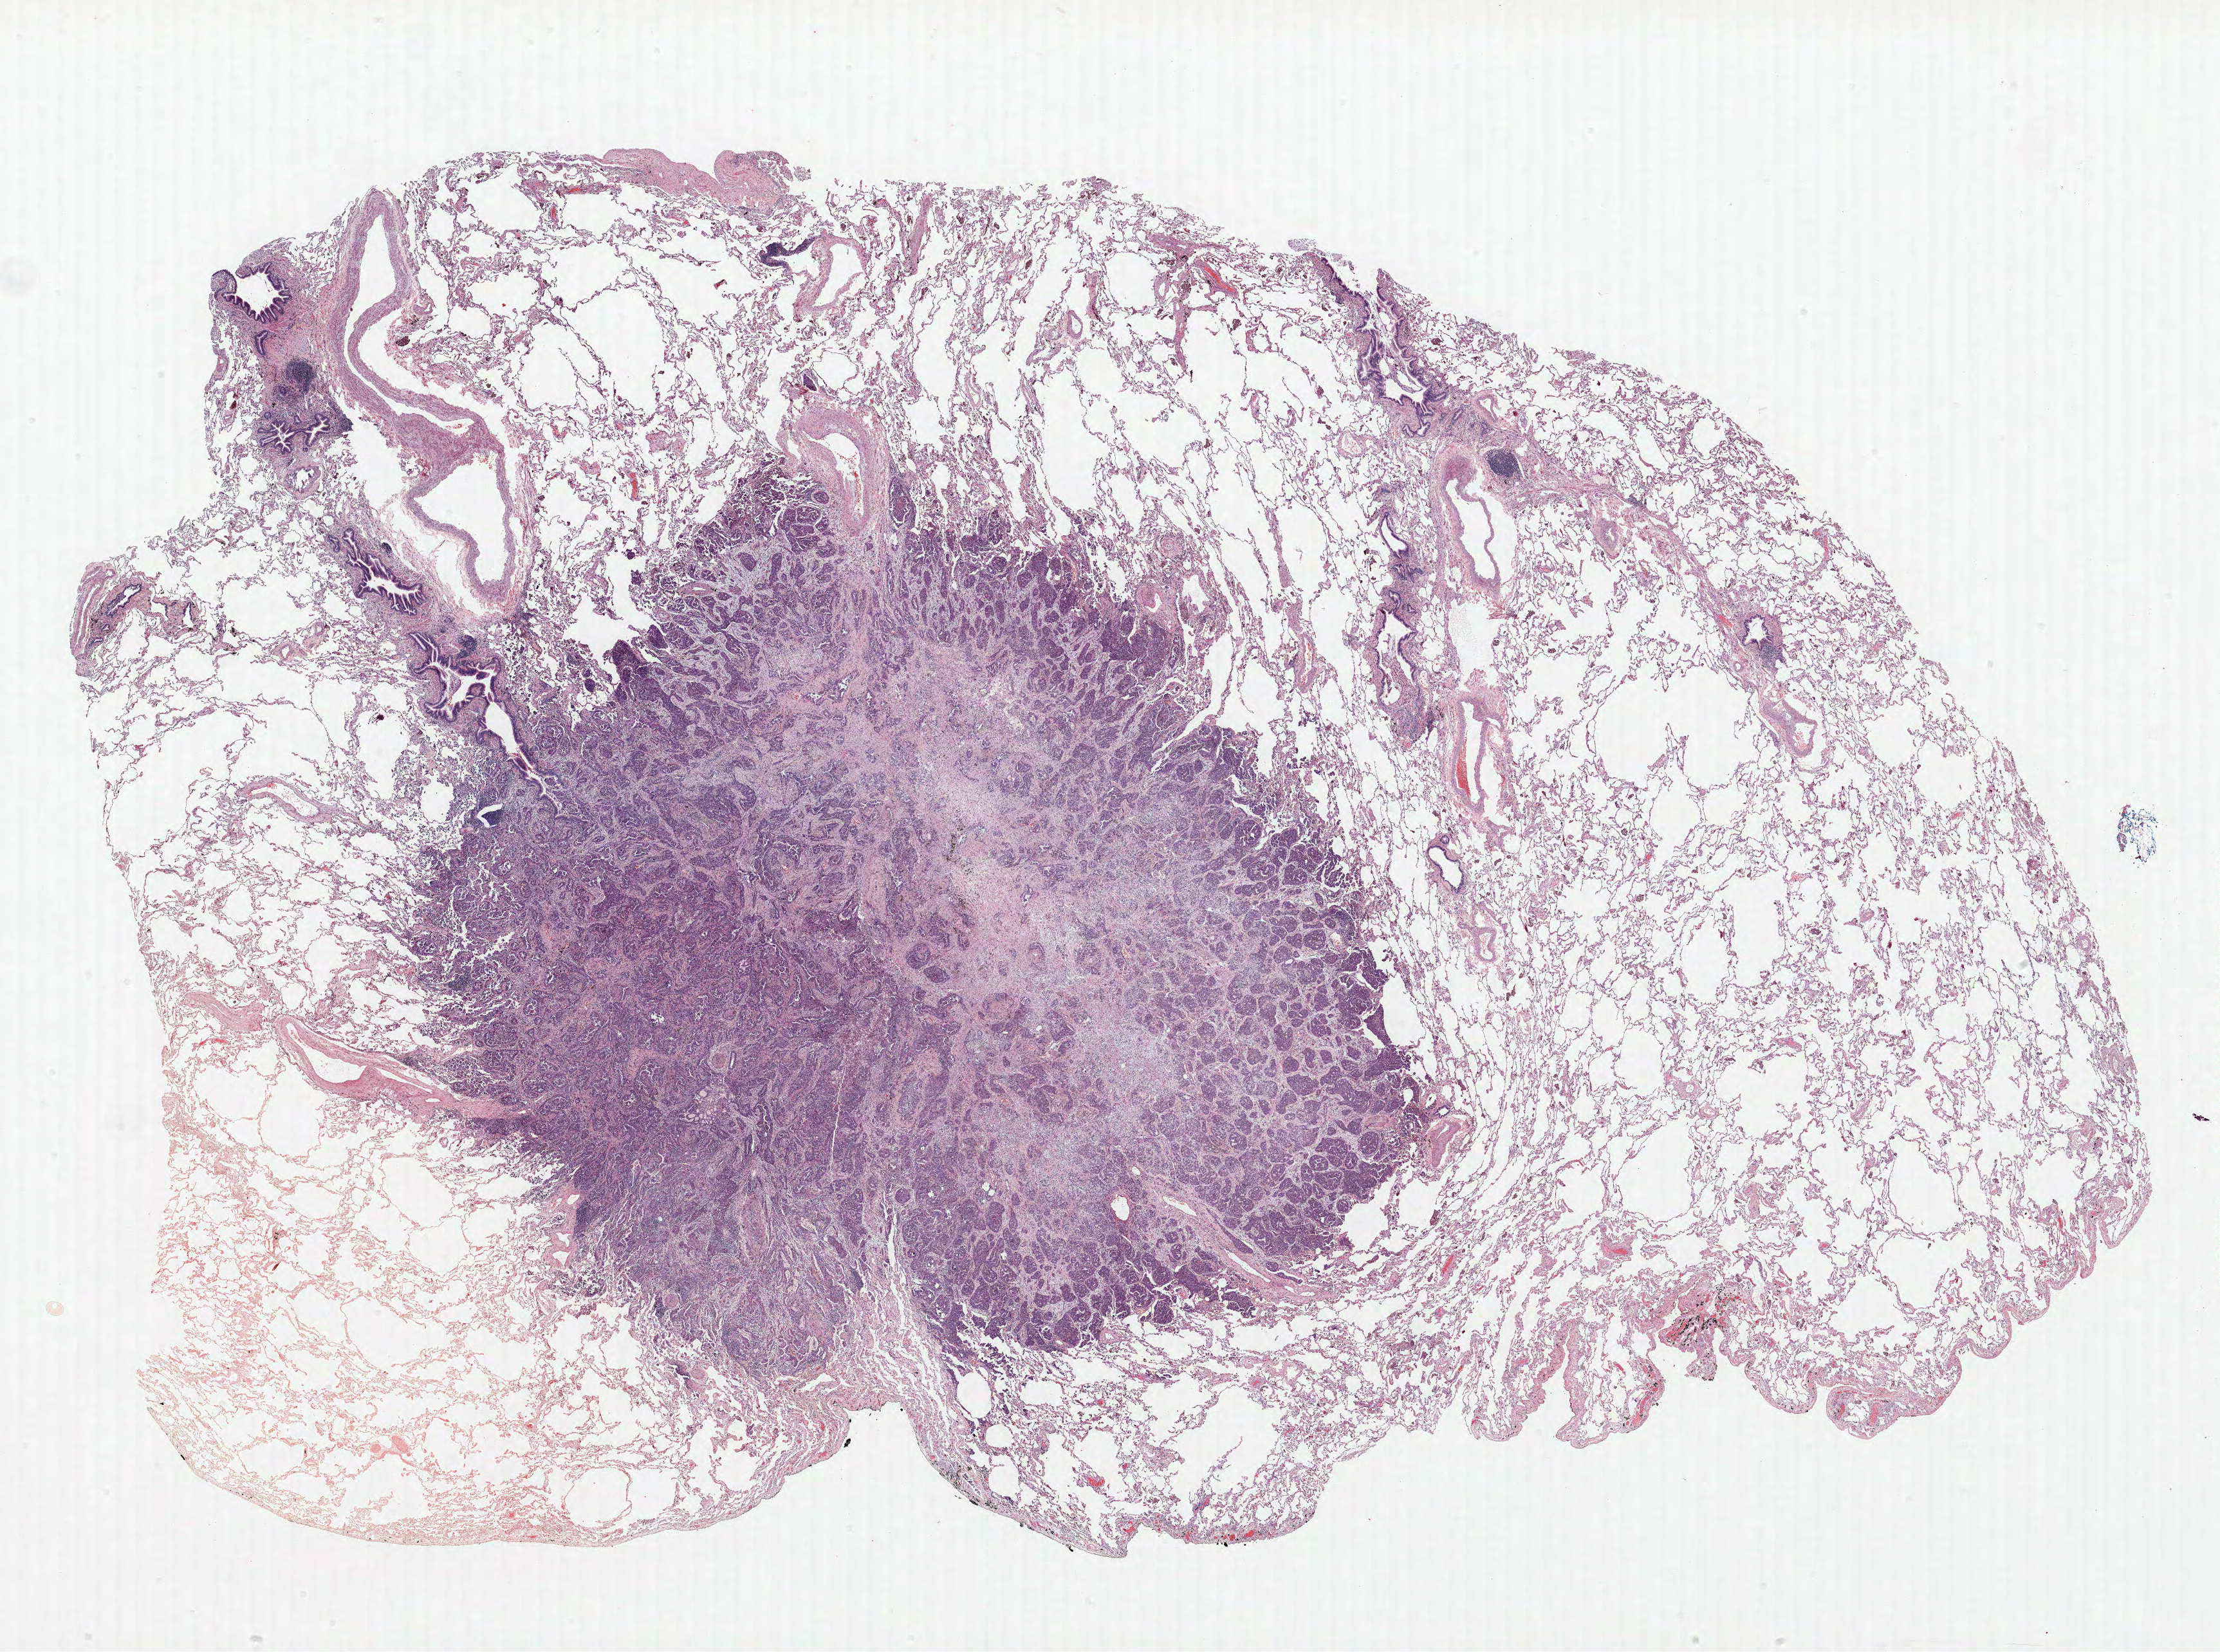
Whole-slide histology image, H&E — low-resolution overview of the scanned area, about 27.6 x 20.5 mm (acquisition: 40x scan); formalin-fixed paraffin-embedded (FFPE) section; lung. Female, age 58 at enrolment. Former smoker at enrolment. Grade: moderately differentiated (G2).
- stage (AJCC 6th edition): IIA
- primary tumour location (clinical record): left upper lobe
- participant's lung-cancer diagnosis: Adenocarcinoma, NOS (ICD-O-3 8140/3)
- tumour size (pathology): 15 mm